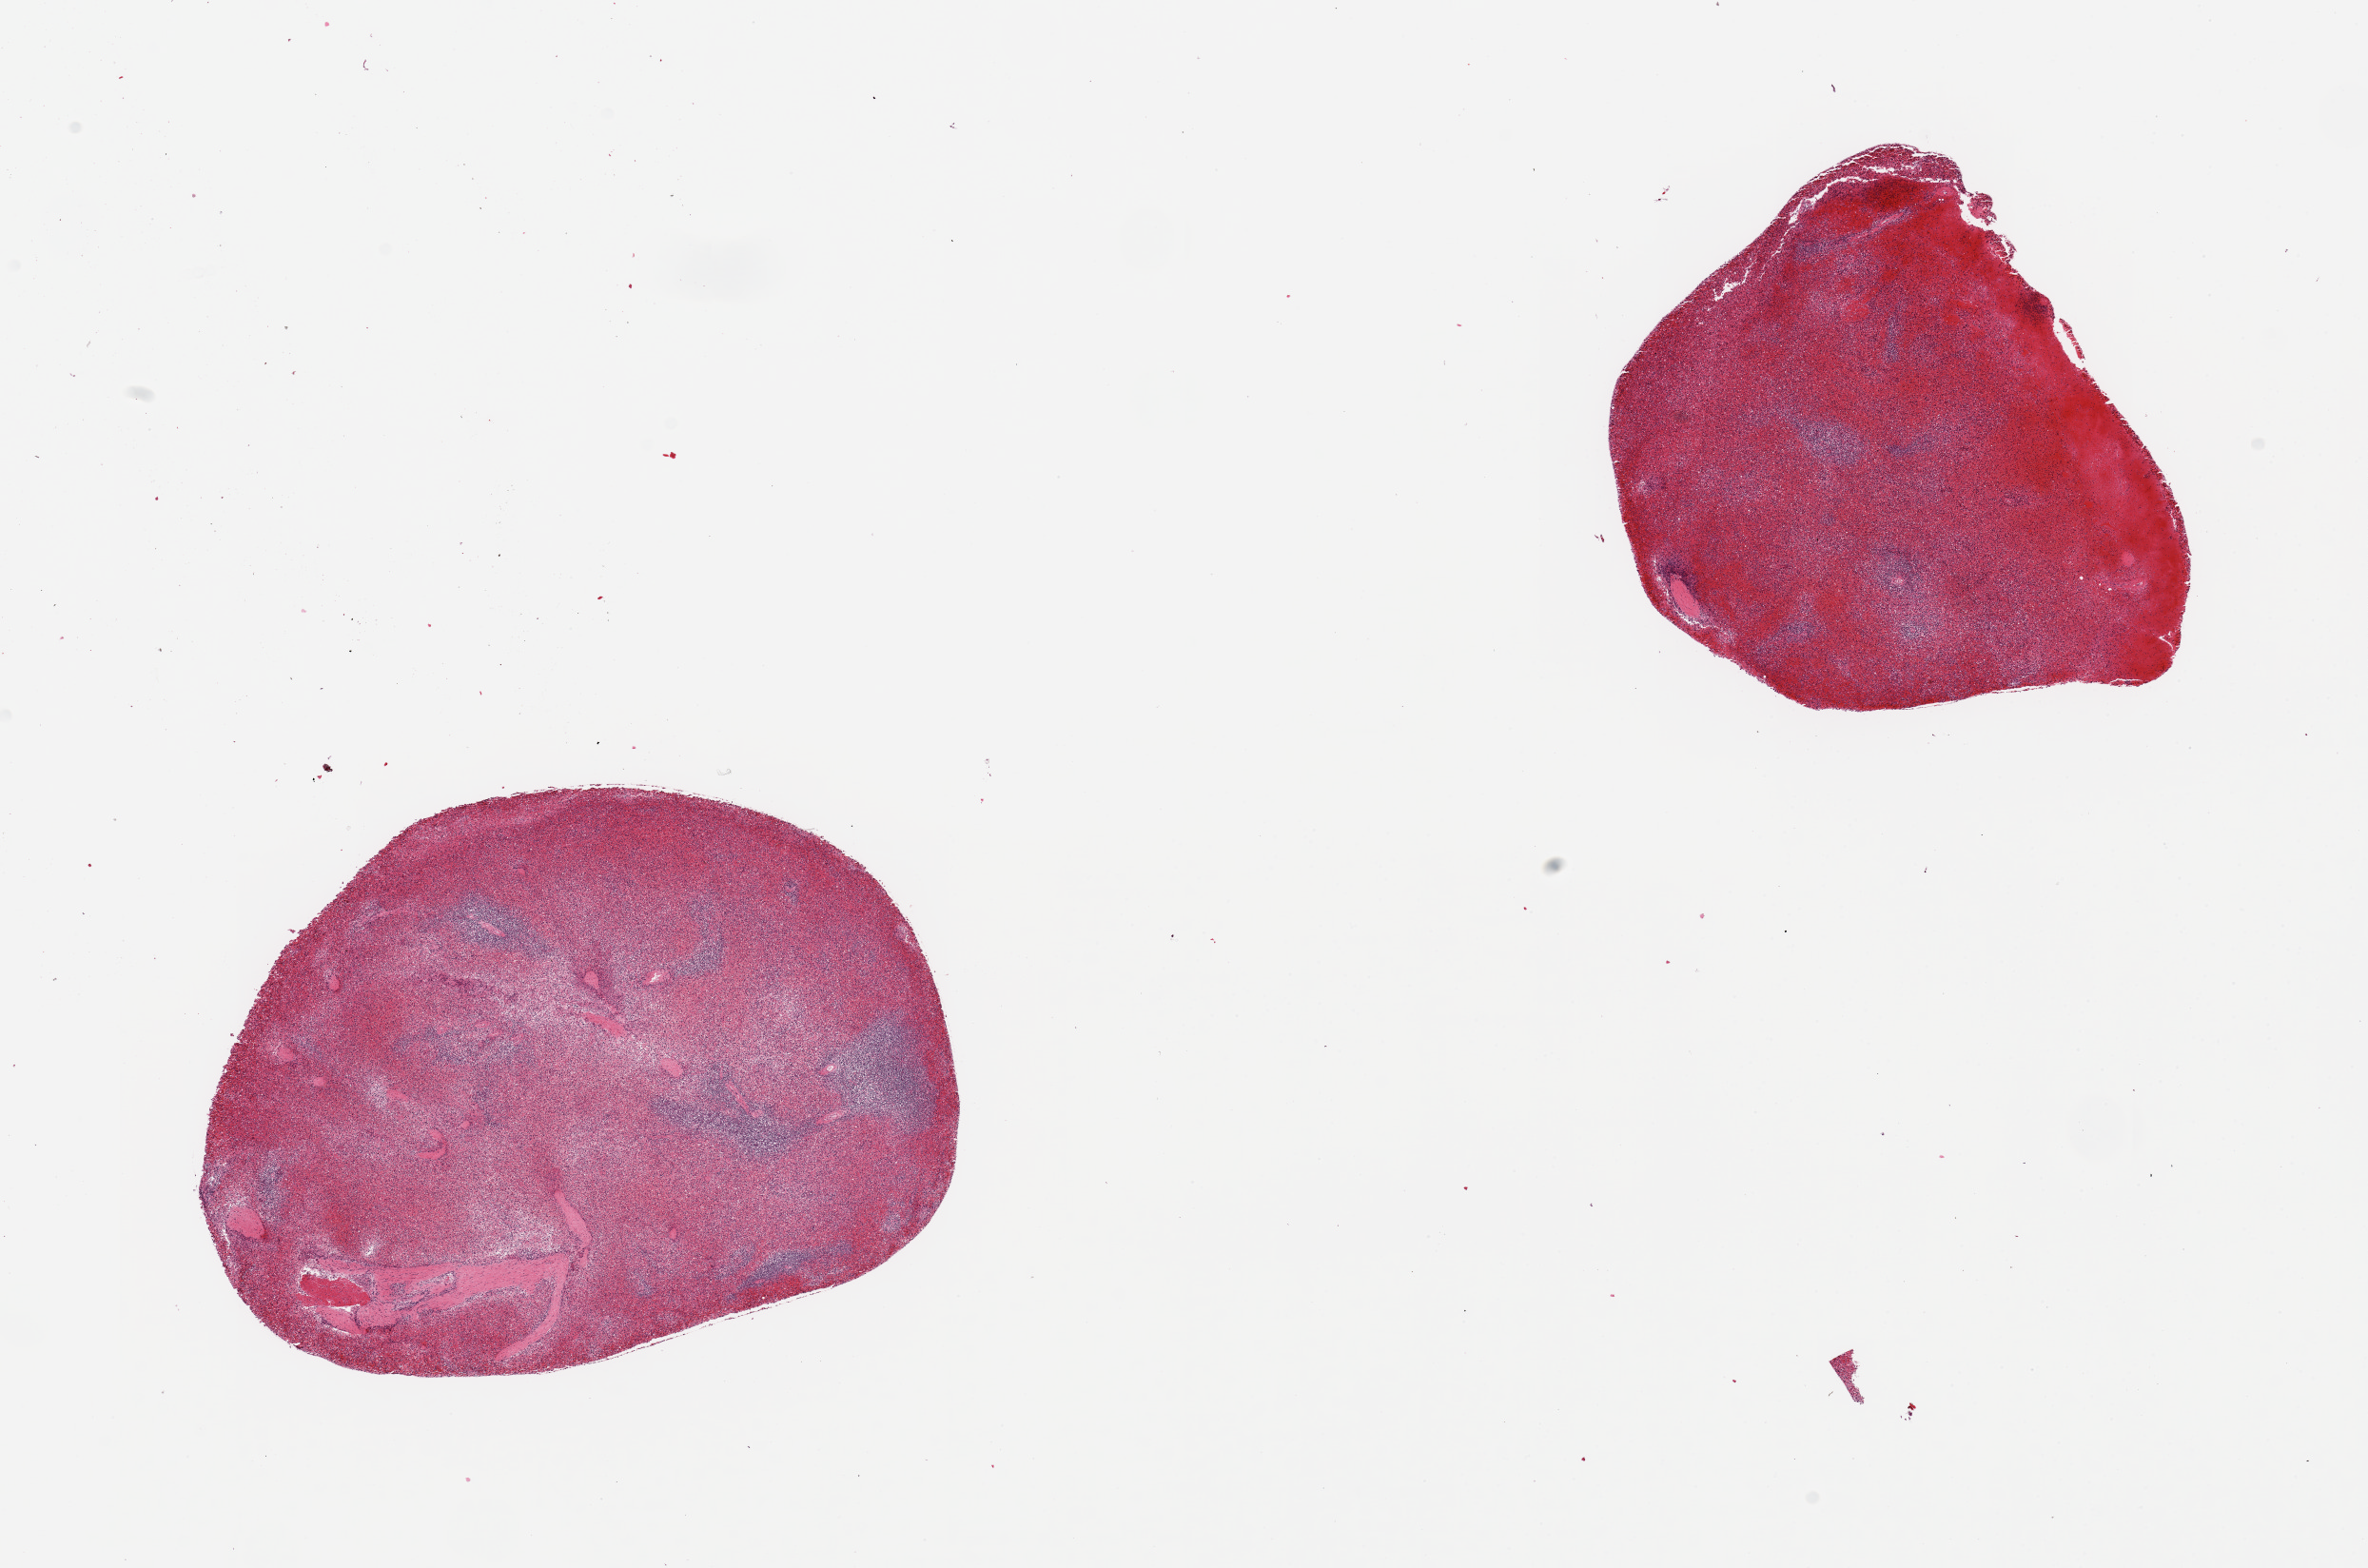
Haematoxylin and eosin whole-slide image, shown as a low-resolution overview of the whole scanned area (about 19.7 x 13.0 mm, acquisition: 20x scan), PAXgene-fixed paraffin-embedded (PFPE) section, section of spleen (target tissue), tissue donor sample. Male donor.
Pathologist's review note for this sample: 2 pieces; congestion.